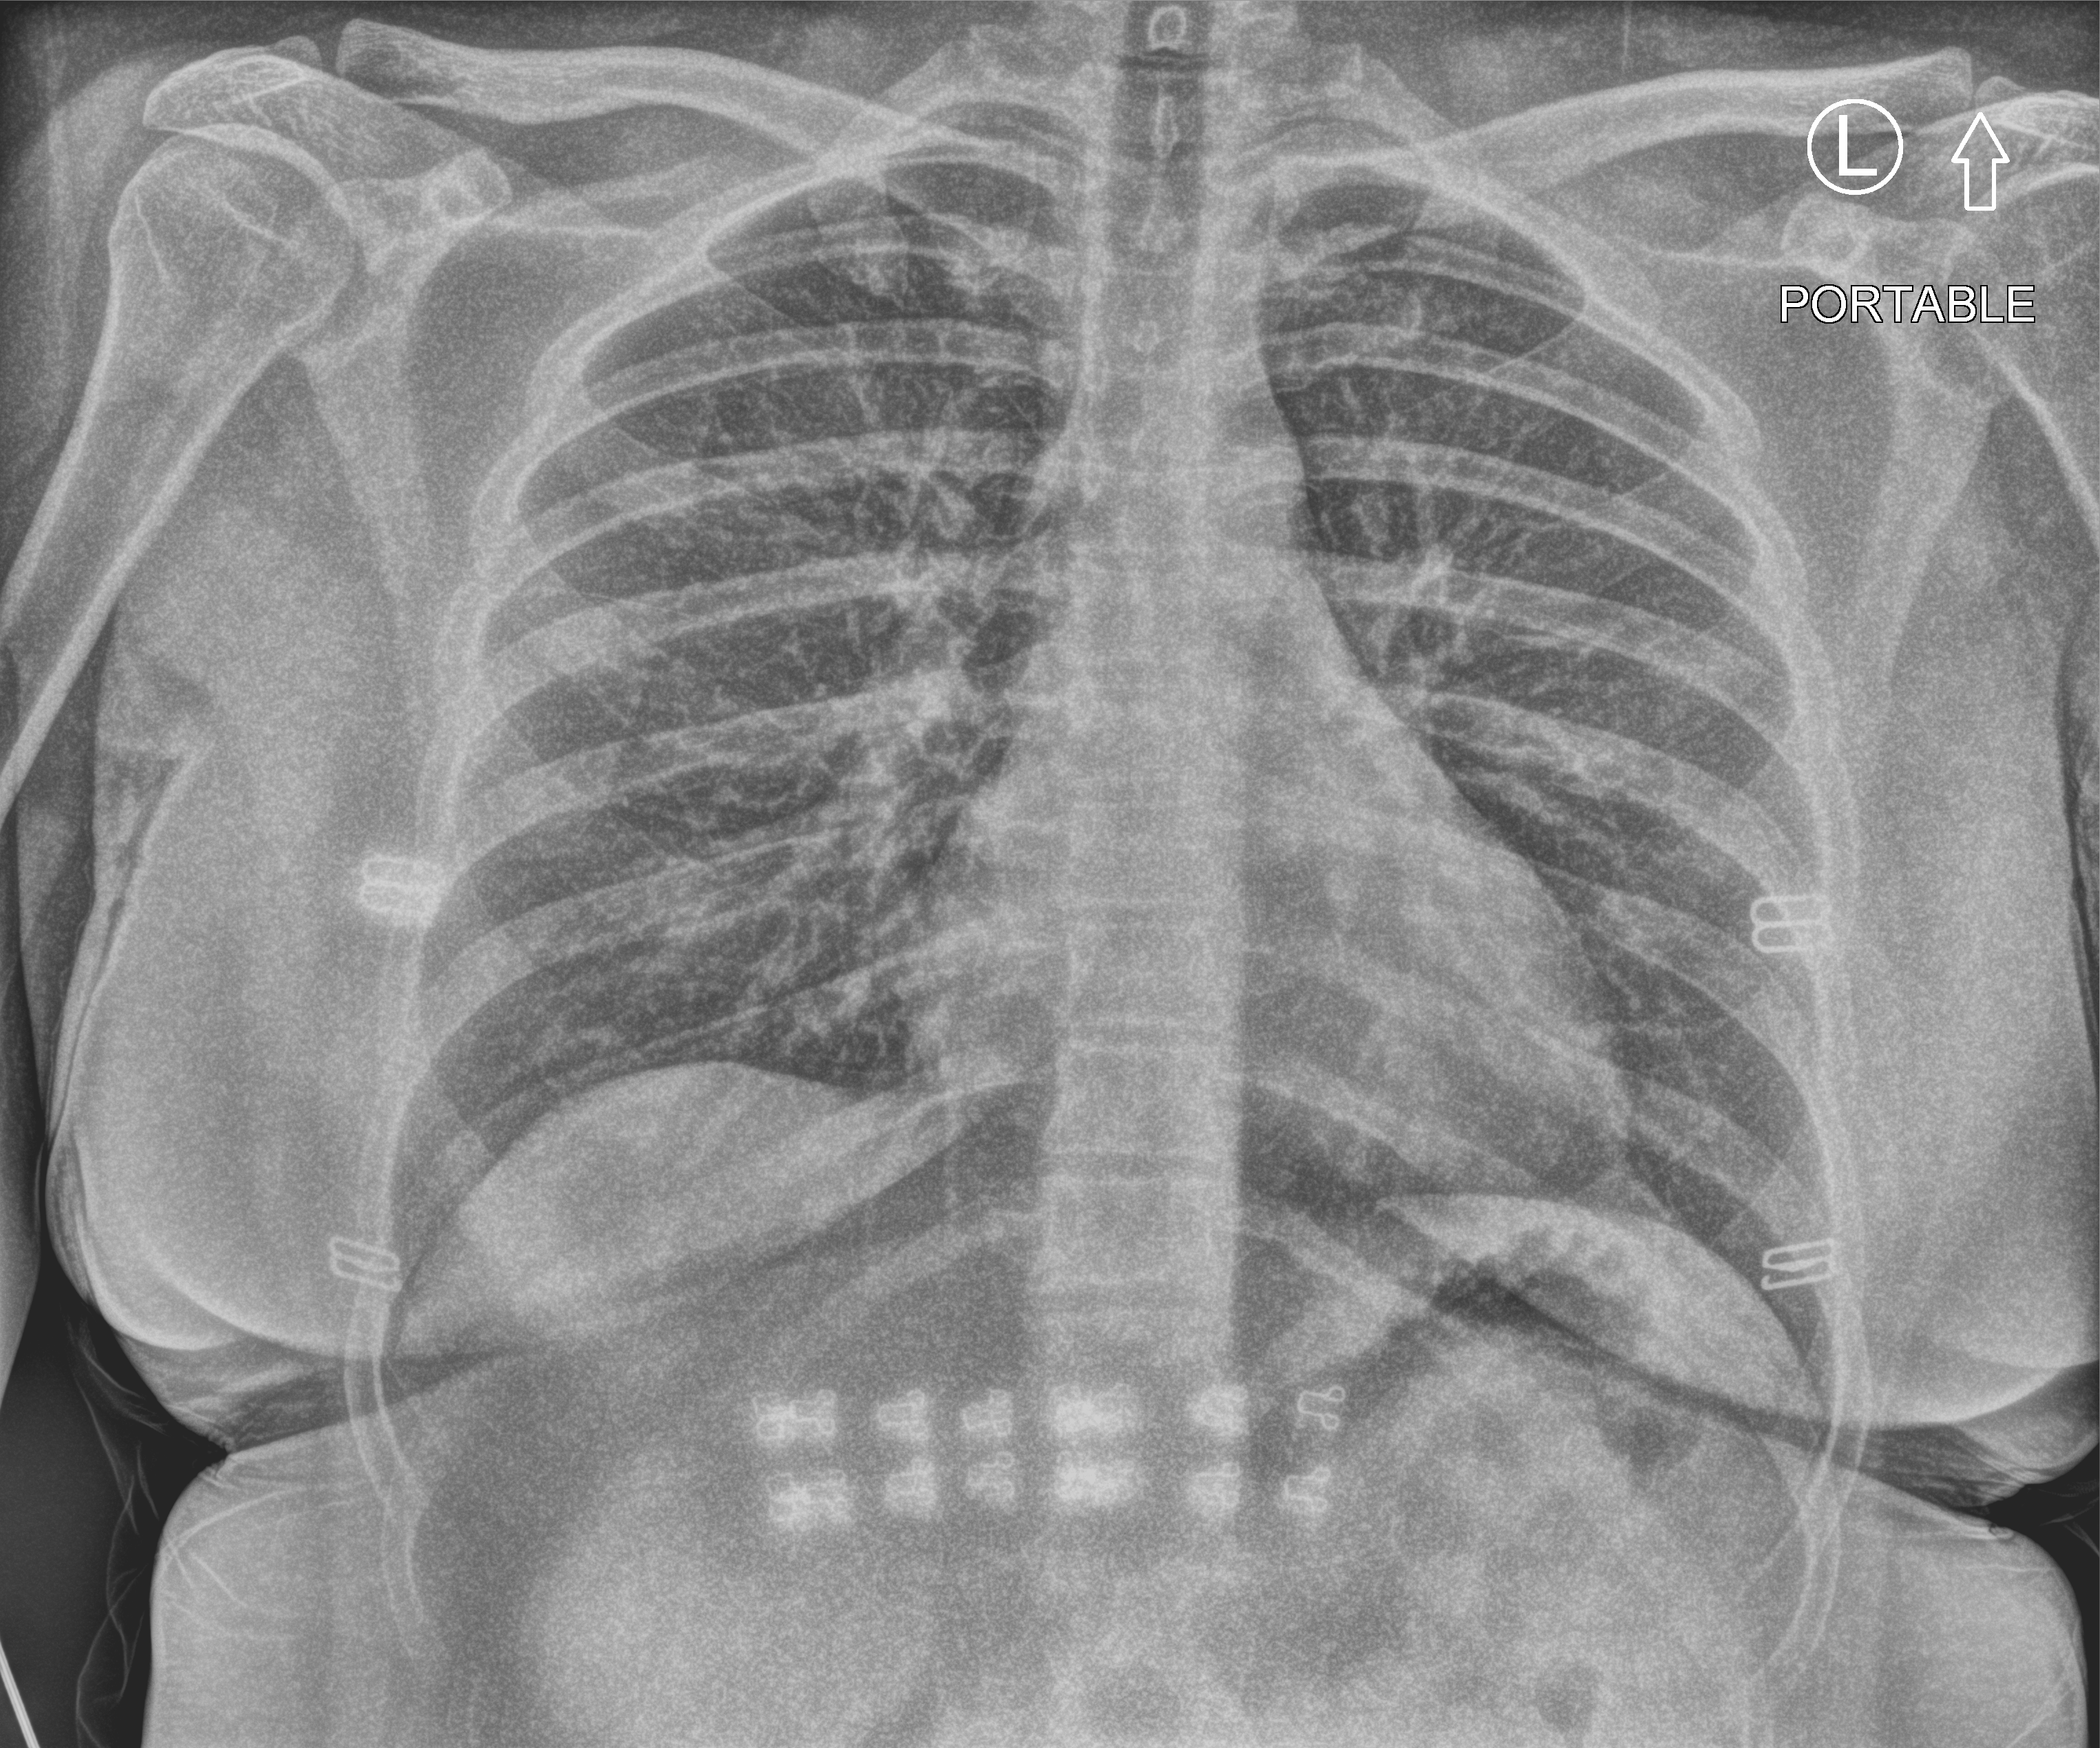
Bedside chest radiograph (computed radiography); anteroposterior (AP) projection. Female patient hospitalised with COVID-19, age 18–59 years.
From the hospital-stay record, not from the radiograph (when in the stay this image was taken is not recorded):
- admitted to intensive care during this hospital stay: no